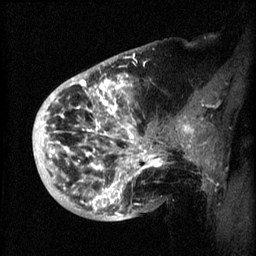
Breast MRI (dynamic contrast-enhanced), one sagittal slice. Slice 17 of 60 in the series (ordered by position). 3 images stored at this slice position (order not interpretable as contrast timing). 1.5 T. TE 4.2 ms, TR 8.2 ms. 2 mm slice thickness. 256 × 256 image matrix. Patient: female, 50 years.
Outlined on this slice (semi-automatic segmentation, software-assisted and operator-edited):
- analysis volume of interest (the breast-tissue region the enhancement analysis was run in; not a lesion): box from (x=44, y=72) to (x=173, y=219) px
- tumour enhancement mask (voxels above the 70 % enhancement threshold inside the analysis volume of interest): (x=52, y=74)–(x=164, y=217)